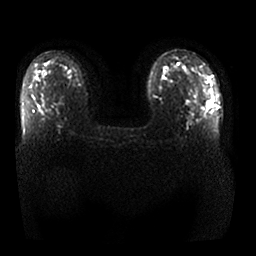
Breast MRI, one axial slice. Slice 15 of 25 in the series (ordered by position). Diffusion-weighted series; image 2 of 4 stored at this slice position (different b-values; order by instance number). 1.5 T. 4 mm slice thickness. 256 × 256 image matrix, field of view 360 × 360 mm. Female patient.
Outlined on this slice (outlined manually by an expert reader):
- tumour on diffusion-weighted imaging: box from (x=207, y=97) to (x=212, y=108) px